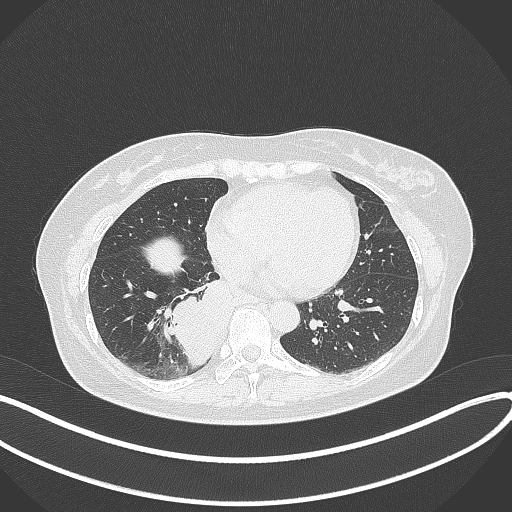
Chest CT, one axial slice. Position 127 of 331 along the scan axis. 120 kVp. Lung window (W 1500 / L -600 HU). 1 mm slice thickness. 512 × 512 image matrix, field of view 400 × 400 mm. Patient: female, 54 years. From the clinical record (not read from this slice): clinical TNM (as recorded): T4 N0 M0.
Annotated regions visible in this slice (bounding box drawn by a radiologist):
- lung tumour (recorded histology: adenocarcinoma): box from (x=159, y=271) to (x=242, y=368) px